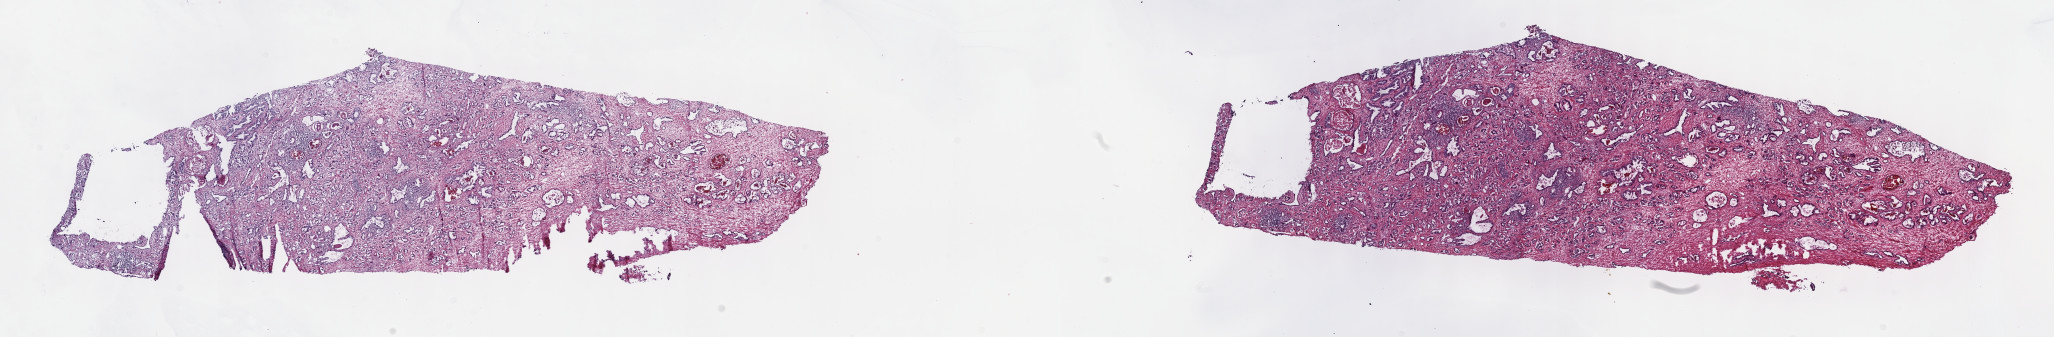
Digitized Hematoxylin and eosin (H&E) stained tissue section (whole slide), shown as a low-resolution overview of the whole scanned area (about 33.2 x 5.5 mm, slide scanned at 40x). Frozen section. Sample: primary tumour, prostate. Male patient; age at initial diagnosis 58 years. Gleason score: 7 (3+4). Pathologist review of this section (percent, as recorded): tumour cells 50%, tumour nuclei 60%, normal cells 20%, stromal cells 30%, necrosis 0%. Infiltration values recorded for this section: lymphocyte infiltration 0%, monocyte infiltration 0%, neutrophil infiltration 0%.
Pathologic diagnosis: Adenocarcinoma, NOS. Lymph nodes positive (case pathology): 1 of 16 examined.